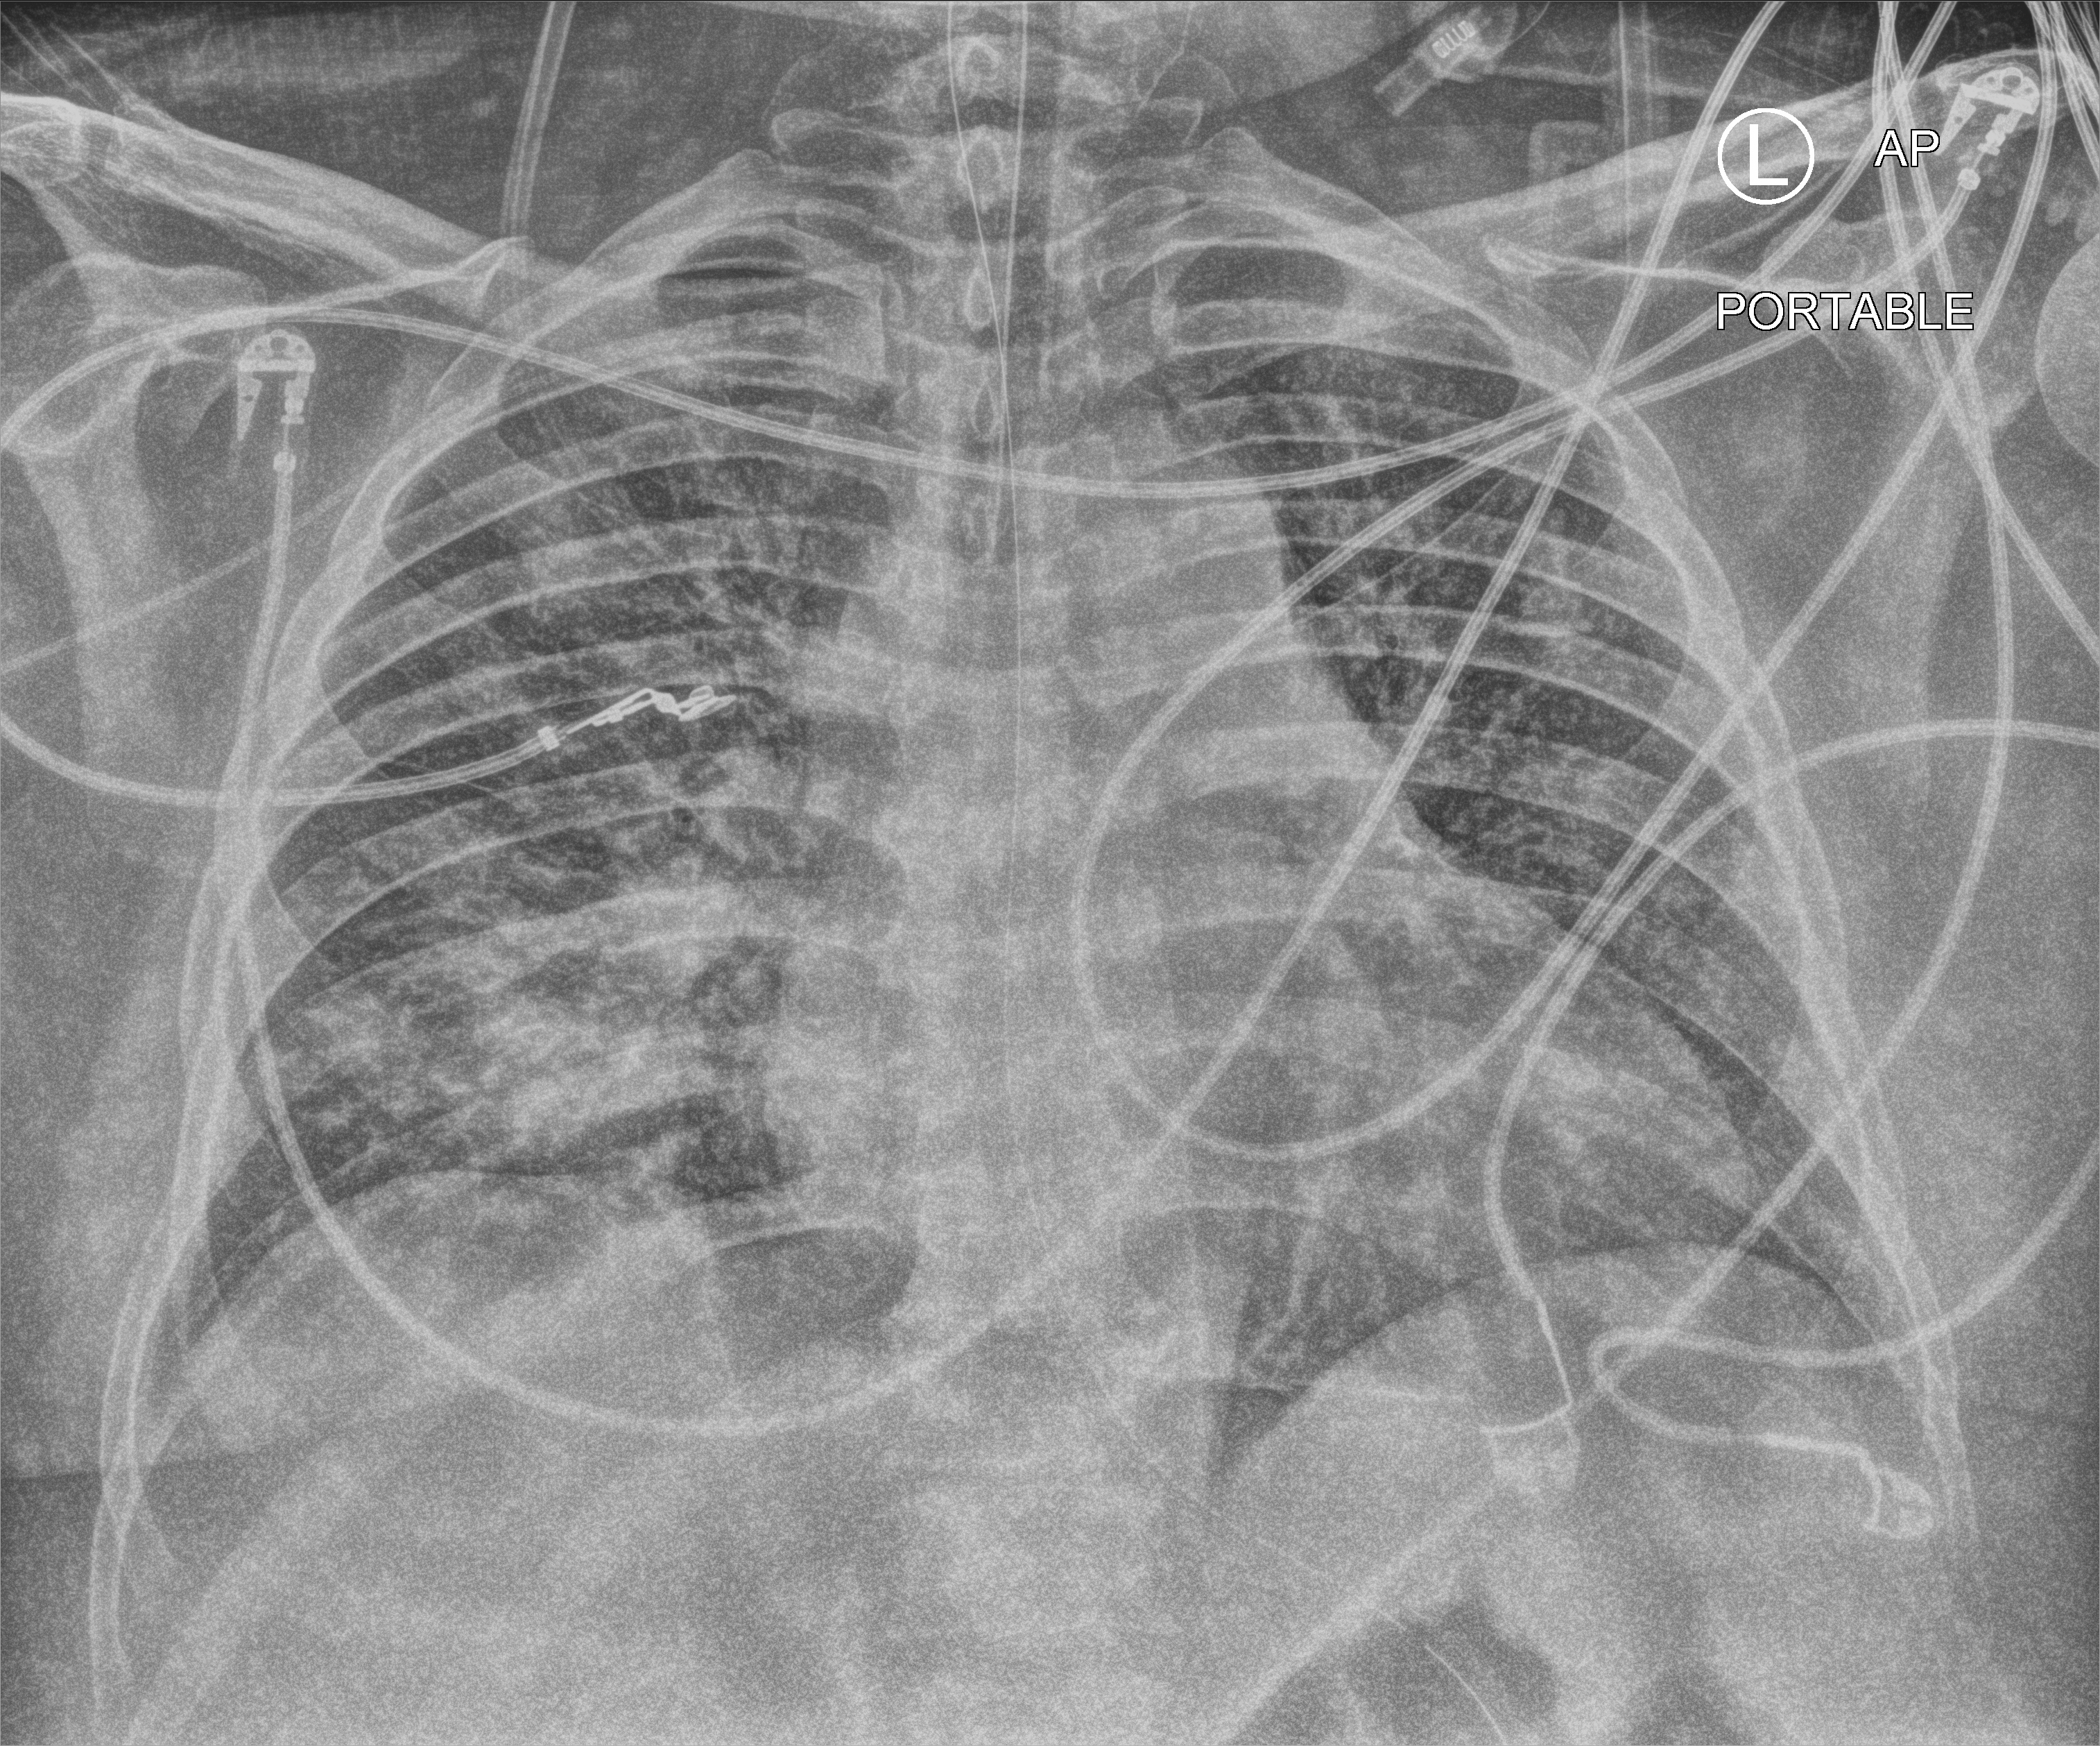
Bedside chest radiograph (computed radiography); anteroposterior (AP) projection. Patient hospitalised with COVID-19; male, aged 18–59 years.
Admission-level facts for this patient (not findings on this image; timing relative to this image not recorded): mechanically ventilated during this hospital stay: yes; smoking status (admission record): never; admitted to intensive care during this hospital stay: yes.